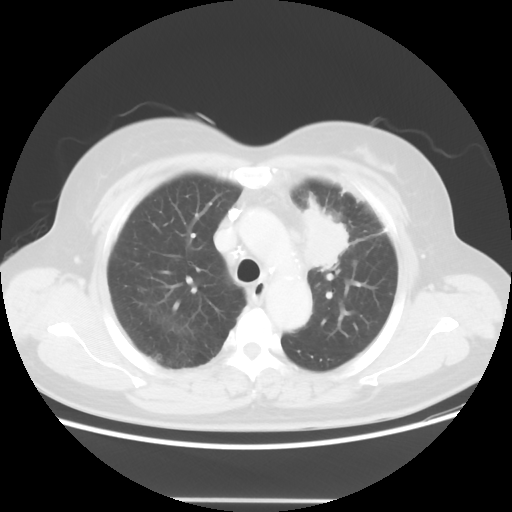
Chest CT, one axial slice. Position 40 of 52 along the scan axis. Reconstruction kernel STANDARD. Lung window (W 1500 / L -600 HU). 5 mm slice thickness. 512 × 512 image matrix, field of view 382 × 382 mm. Patient: female, 52 years. From the clinical record (not read from this slice): clinical TNM (as recorded): T2 N3 M0.
Outlined on this slice (rectangle marked by the reading radiologist):
- lung tumour (recorded histology: adenocarcinoma): bounding box (x1, y1, x2, y2) in pixels: (289, 188, 359, 278)